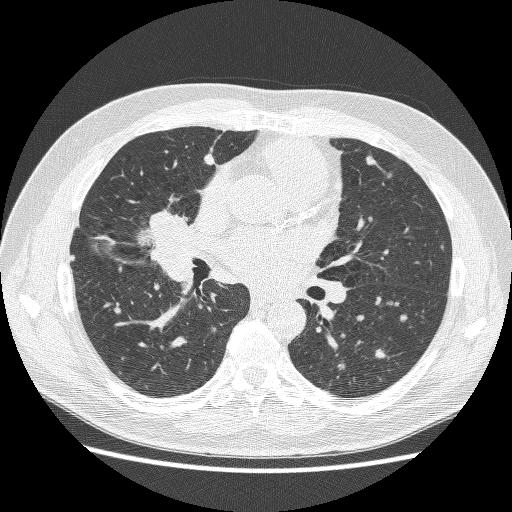
Low-dose screening chest CT, axial slice; baseline annual screen; lung window (W 1500 / L -600 HU); 1.25 mm slice thickness; 120 kVp; slice 144 of 251 in the series. Male participant, aged 59 years at enrolment. Former smoker at enrolment.
Expert reader's lesion annotation, bounding box [x1, y1, x2, y2] px = [126, 200, 198, 268]. Screening reader's record for this exam: no non-calcified nodule ≥4 mm recorded. Official screen result: positive, change unspecified: nodule(s) >= 4 mm or enlarging nodule(s), mass(es), or other non-specific abnormalities suspicious for lung cancer.